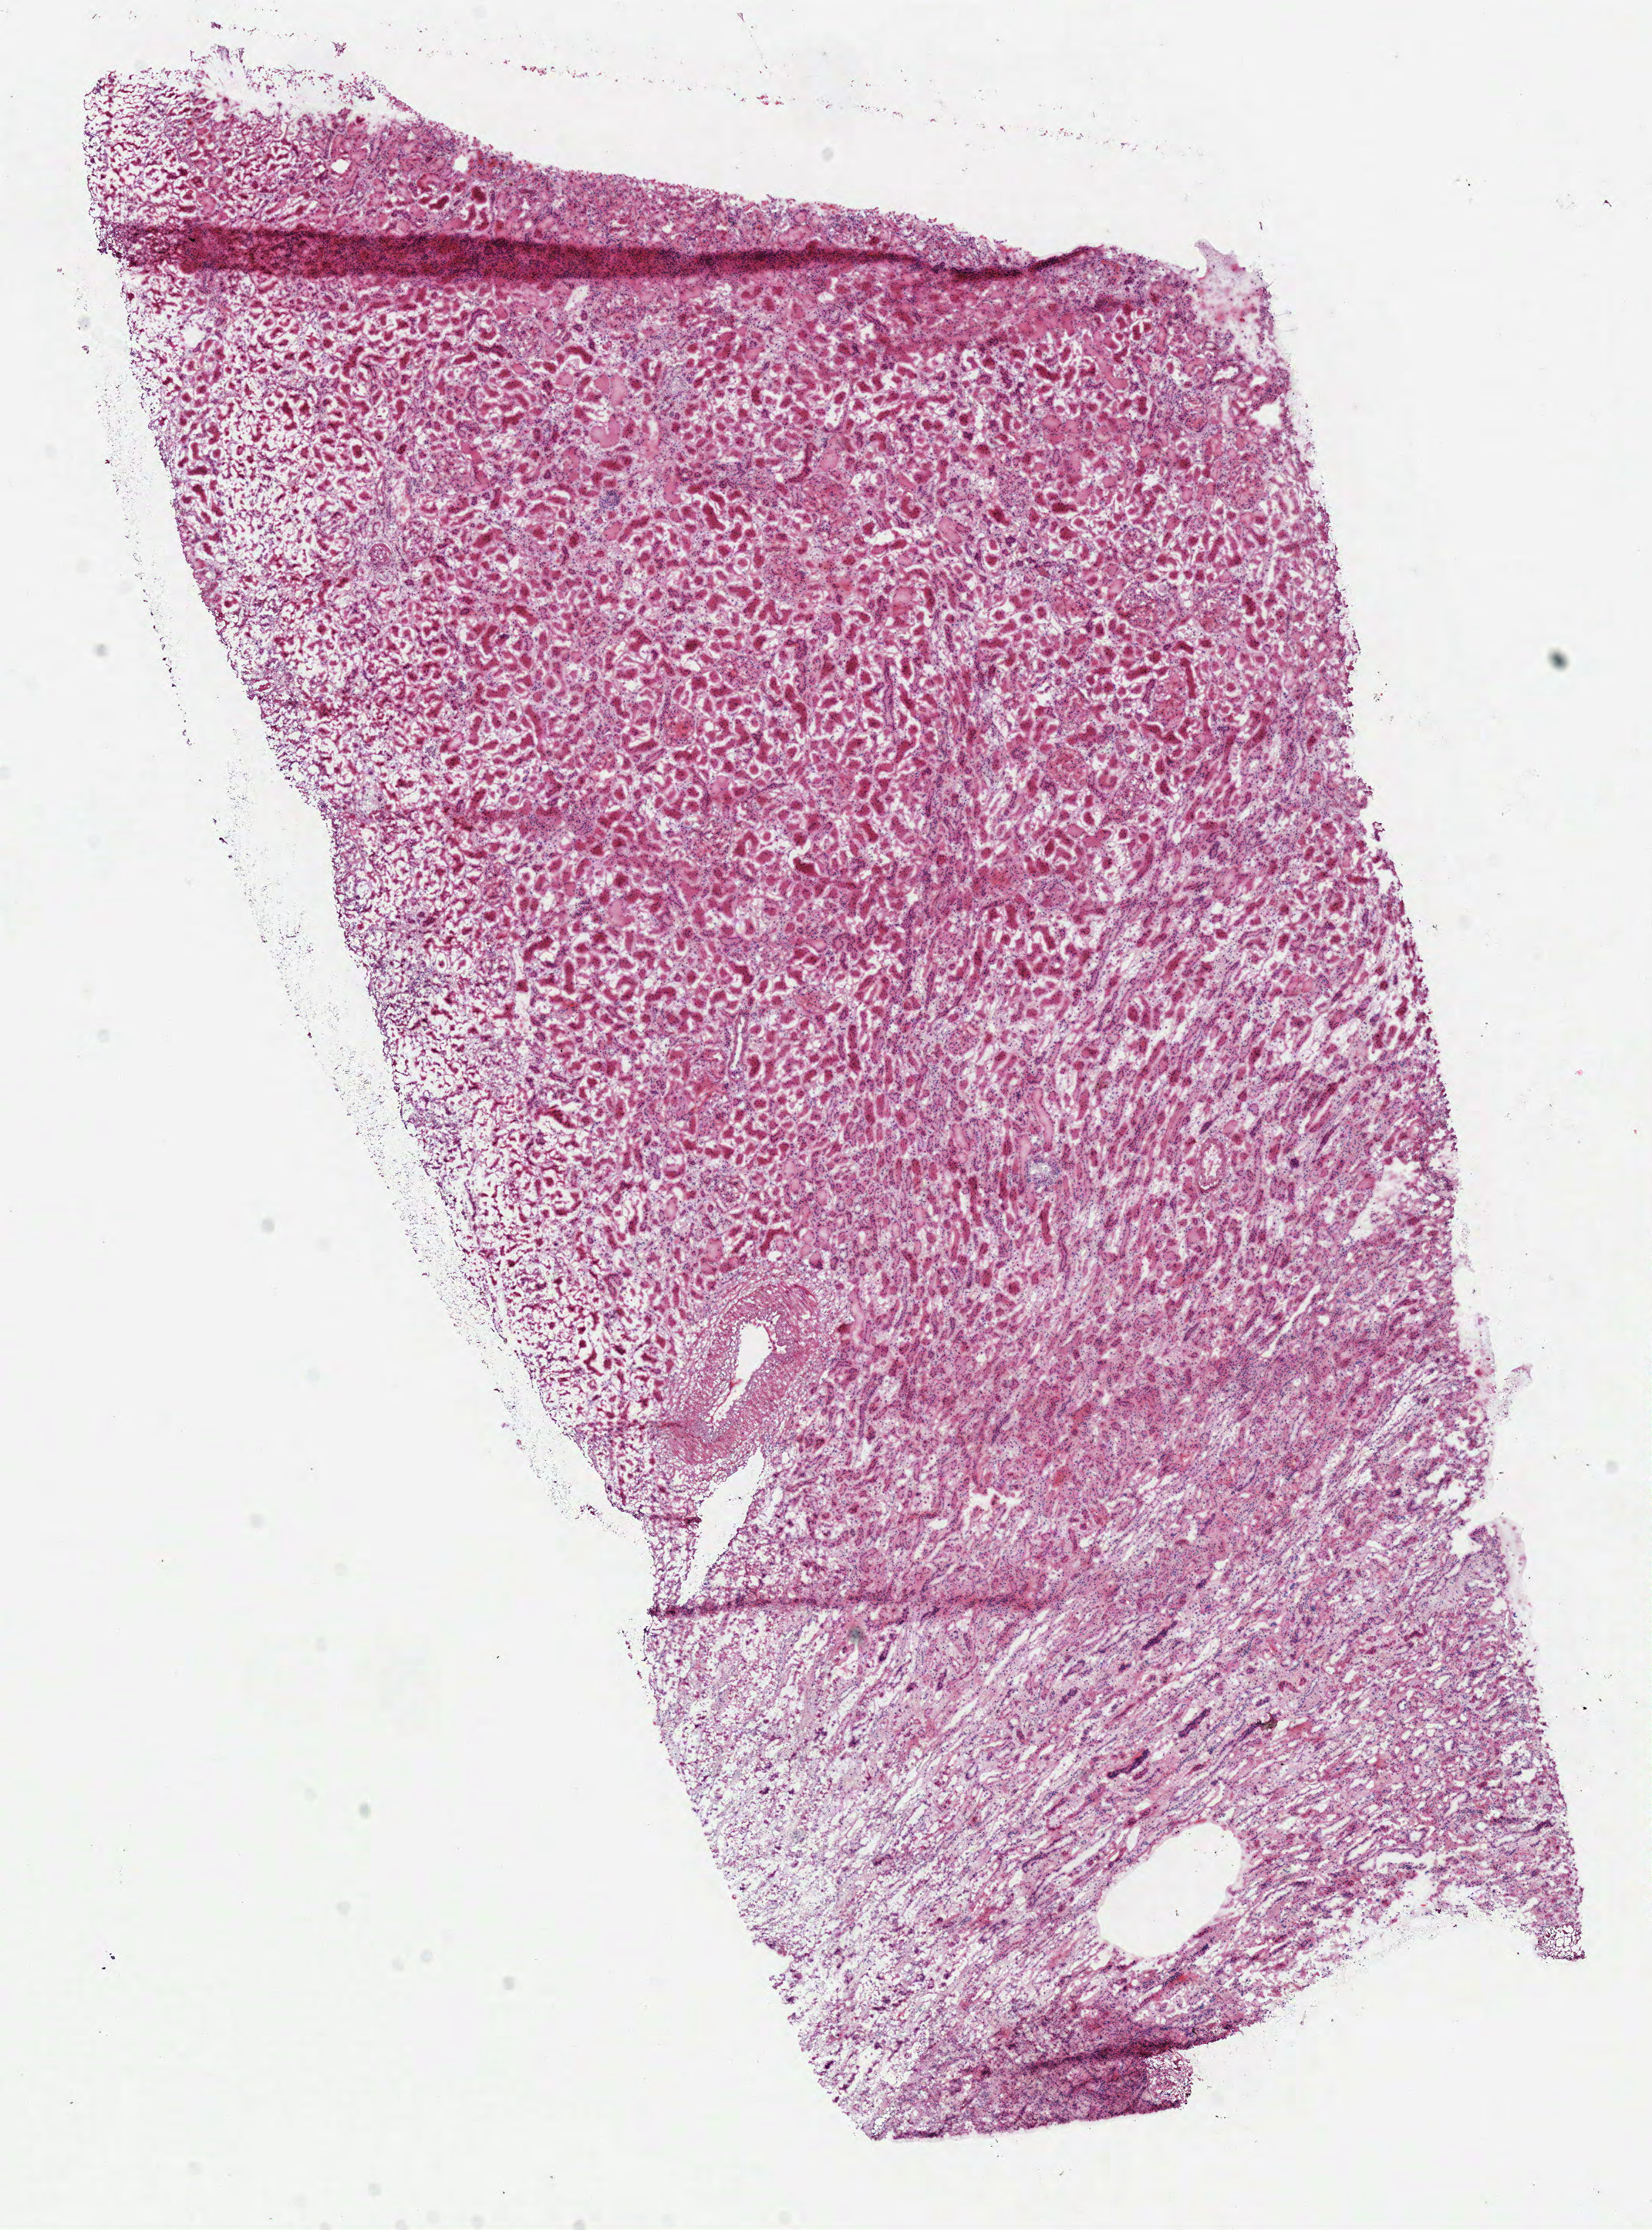
H&E-stained whole-slide image — whole scanned area (about 8.4 x 11.4 mm, slide scanned at 40x) shown as a low-resolution overview. Frozen section from the top of the tissue portion. Sample: solid tissue normal (non-tumour tissue), kidney. Male patient; age at initial diagnosis 61 years.
• this section: solid tissue normal (non-tumour) sample from the same patient
• patient diagnosis: Clear cell adenocarcinoma, NOS